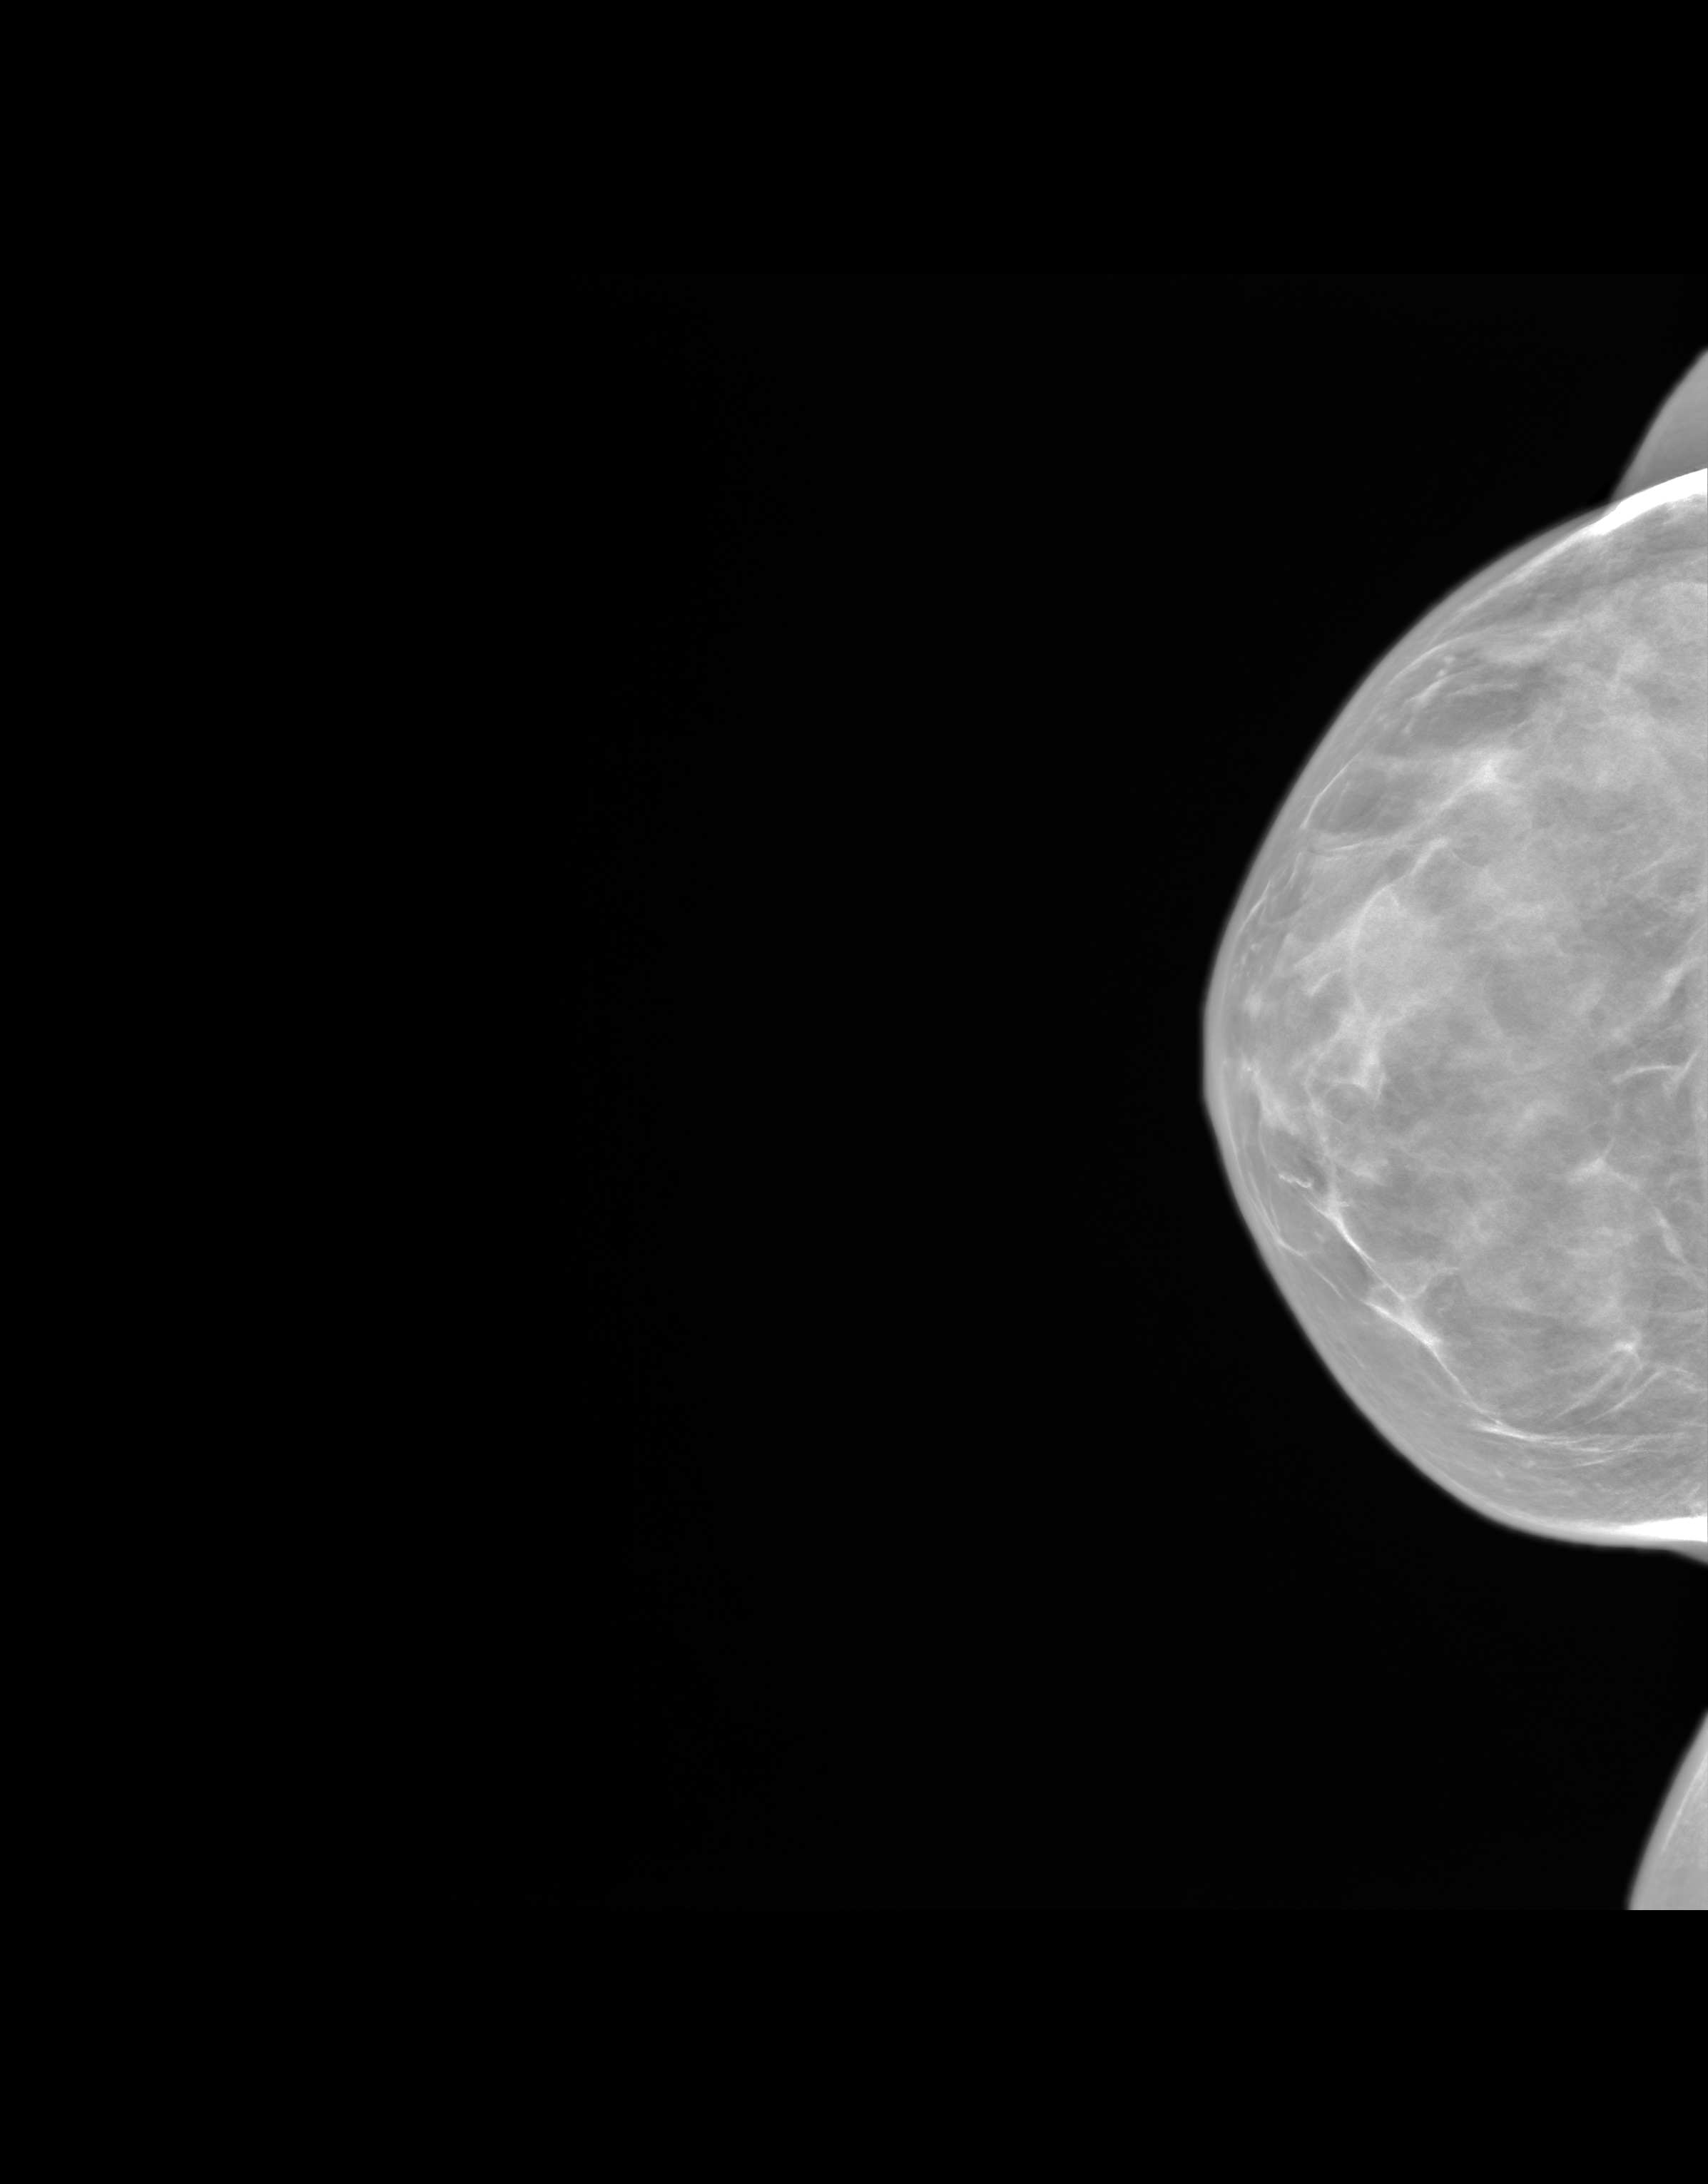
Synthesized 2-D mammogram reconstructed from digital breast tomosynthesis, right breast, craniocaudal (CC) view, screening examination. Female patient, age 66 years.
Breast density at the screening exam (both breasts): heterogeneously dense (BI-RADS density category c). Final BI-RADS assessment for this screening round (tomosynthesis exam, both breasts): category 1. Recall: no recall after this screen.